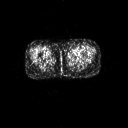
FDG PET of an extremity soft-tissue mass (from a PET/CT study), one axial slice. Slice 2 of 267 in the series (ordered by position). 3.27 mm slice thickness. 128 × 128 image matrix, field of view 700 × 700 mm. Patient: female, 47 years. Case-level facts recorded for this patient, not image findings: histological type: myxofibrosarcoma; grade: intermediate; site of the primary tumour: left thigh.
Structures marked on this image (expert contour drawn on MRI and transferred to this co-registered scan by the dataset authors):
- gross tumour volume including surrounding oedema: bounding box (x1, y1, x2, y2) in pixels: (70, 55, 80, 60)